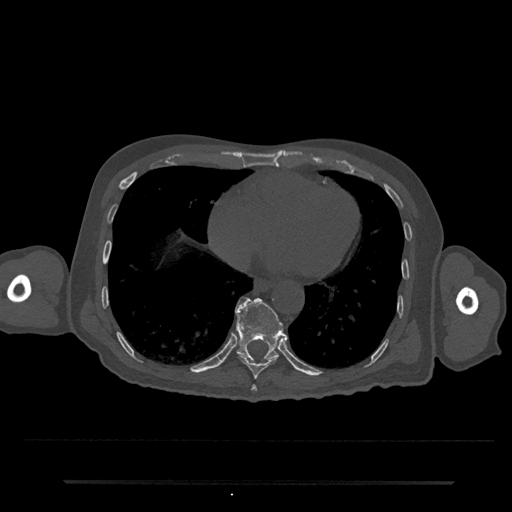
CT including the spine, one axial slice. Position 342 of 797 along the scan axis. Reconstruction kernel Br40s/3. 120 kVp. Bone window (W 1800 / L 400 HU). 512 × 512 image matrix, field of view 427 × 427 mm. Male patient, age 74 years. From the clinical record (not read from this slice): primary cancer: prostate.
Annotated regions visible in this slice (semi-automatic segmentation, software-assisted and operator-edited):
- T10 vertebra: bounding box (x1, y1, x2, y2) in pixels: (235, 297, 285, 361)
- T8 vertebra: (251, 385, 258, 391)
- T9 vertebra: (238, 354, 278, 380)